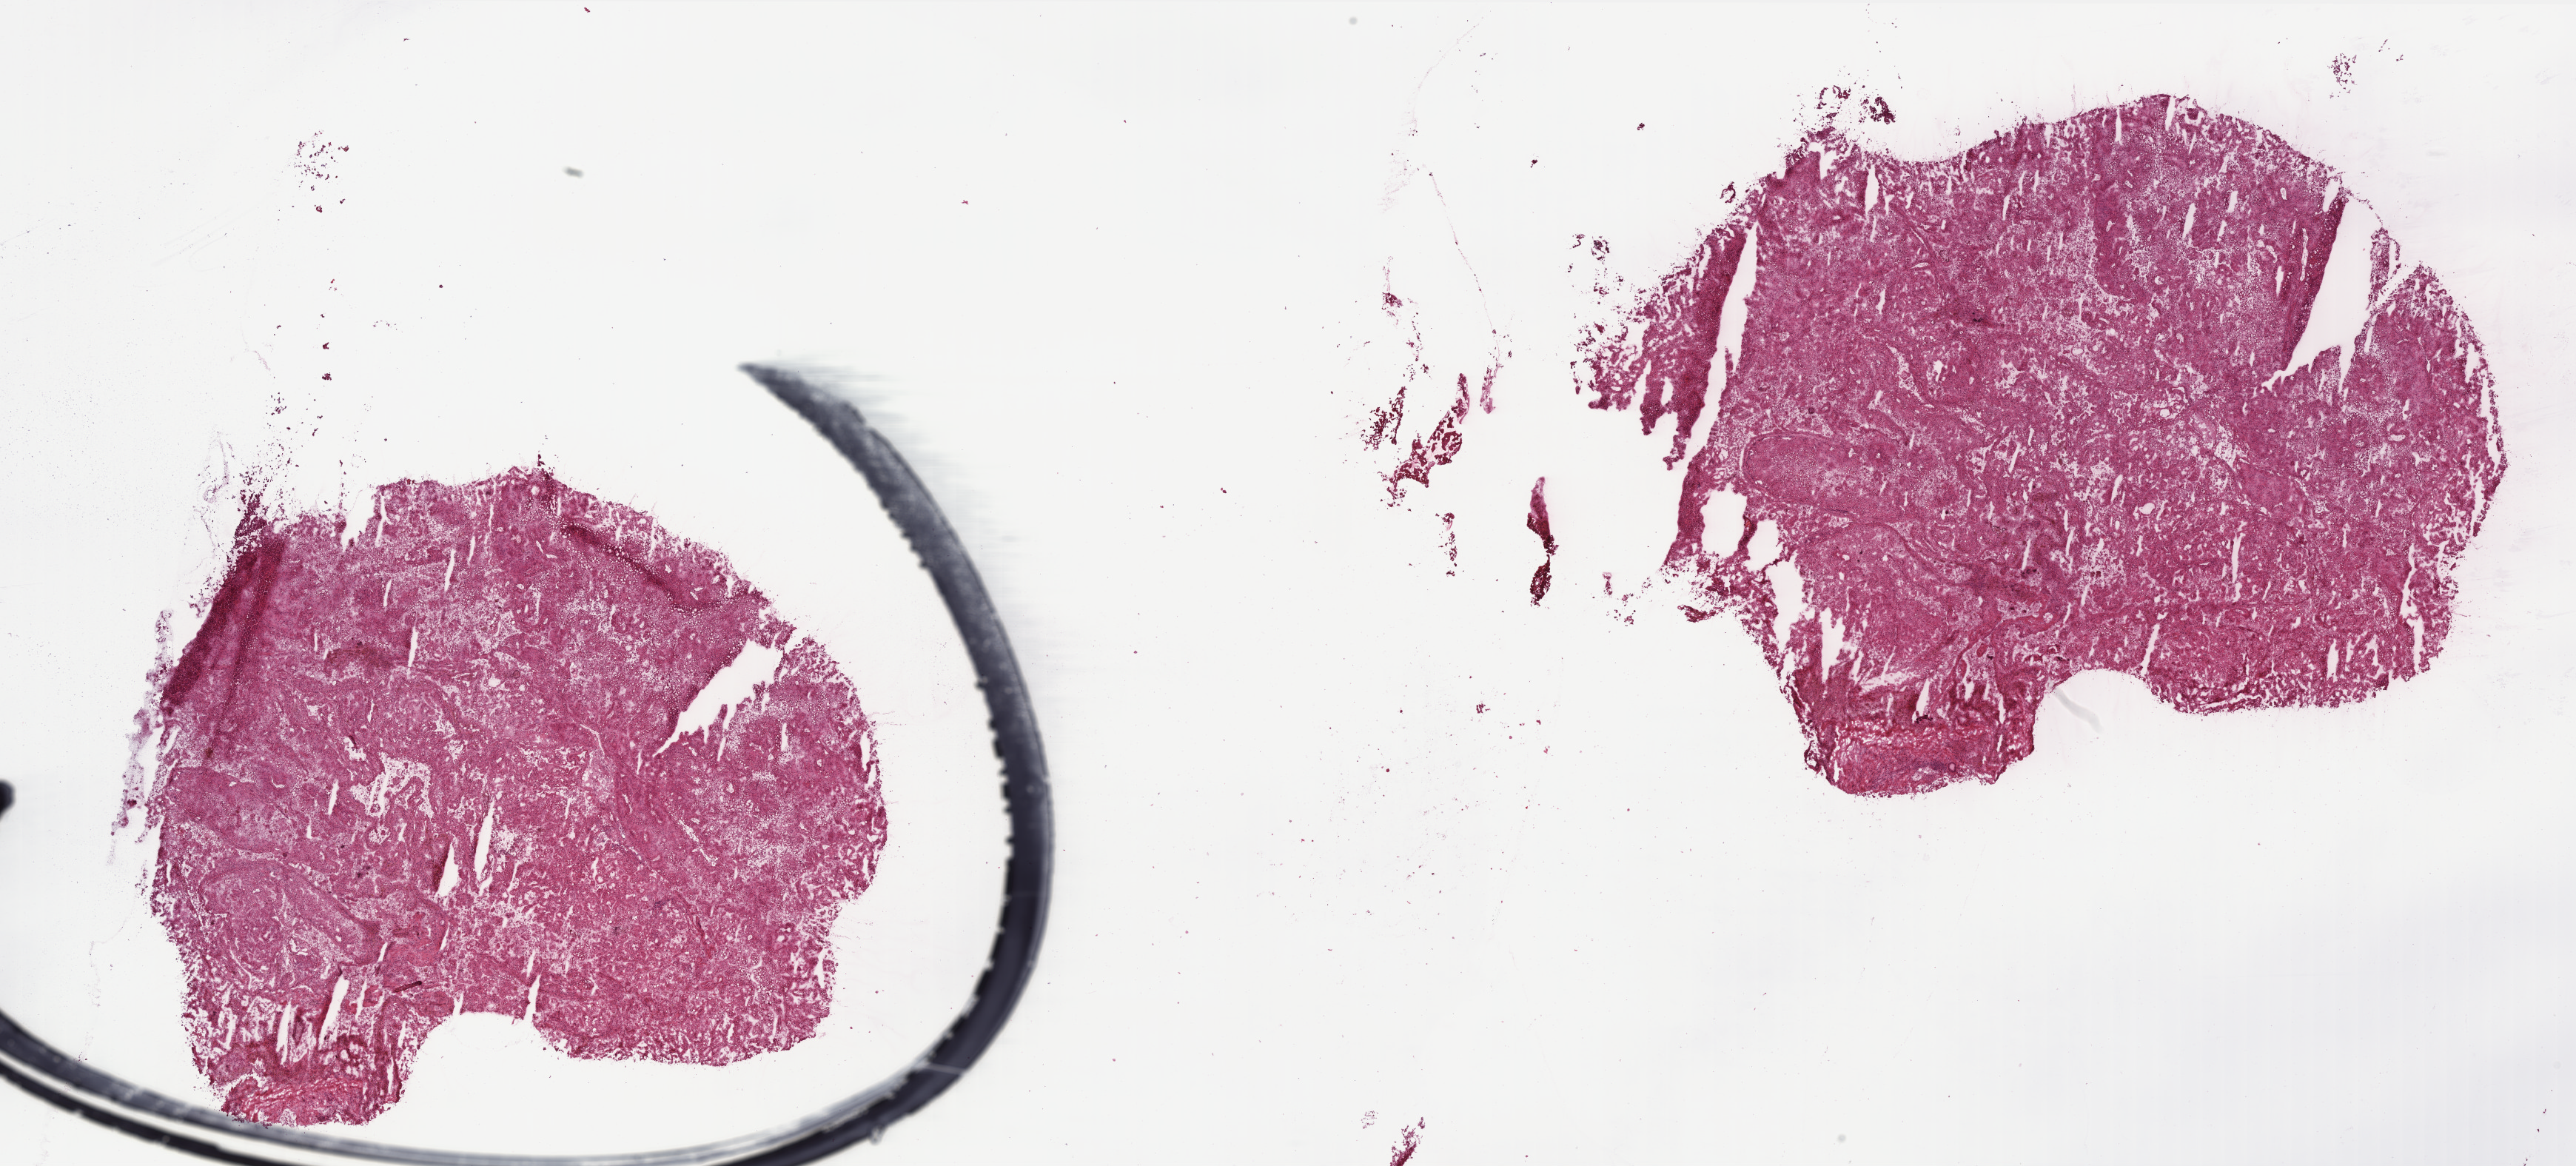
Whole-slide histology image, Hematoxylin and eosin (H&E) stained, whole scanned area (about 27.9 x 12.6 mm, slide scanned at 40x) shown as a low-resolution overview, frozen section from the top of the tissue portion, primary tumour sample from the kidney. Female patient; age at initial diagnosis 51 years. Pathologist review of this section (percent, as recorded): tumour cells 100%, tumour nuclei 65%, normal cells 0%, stromal cells 0%, necrosis 0%. Inflammatory infiltration, as recorded: lymphocyte infiltration 2%, monocyte infiltration 8%, neutrophil infiltration 0%.
Histologic diagnosis: Papillary adenocarcinoma, NOS.